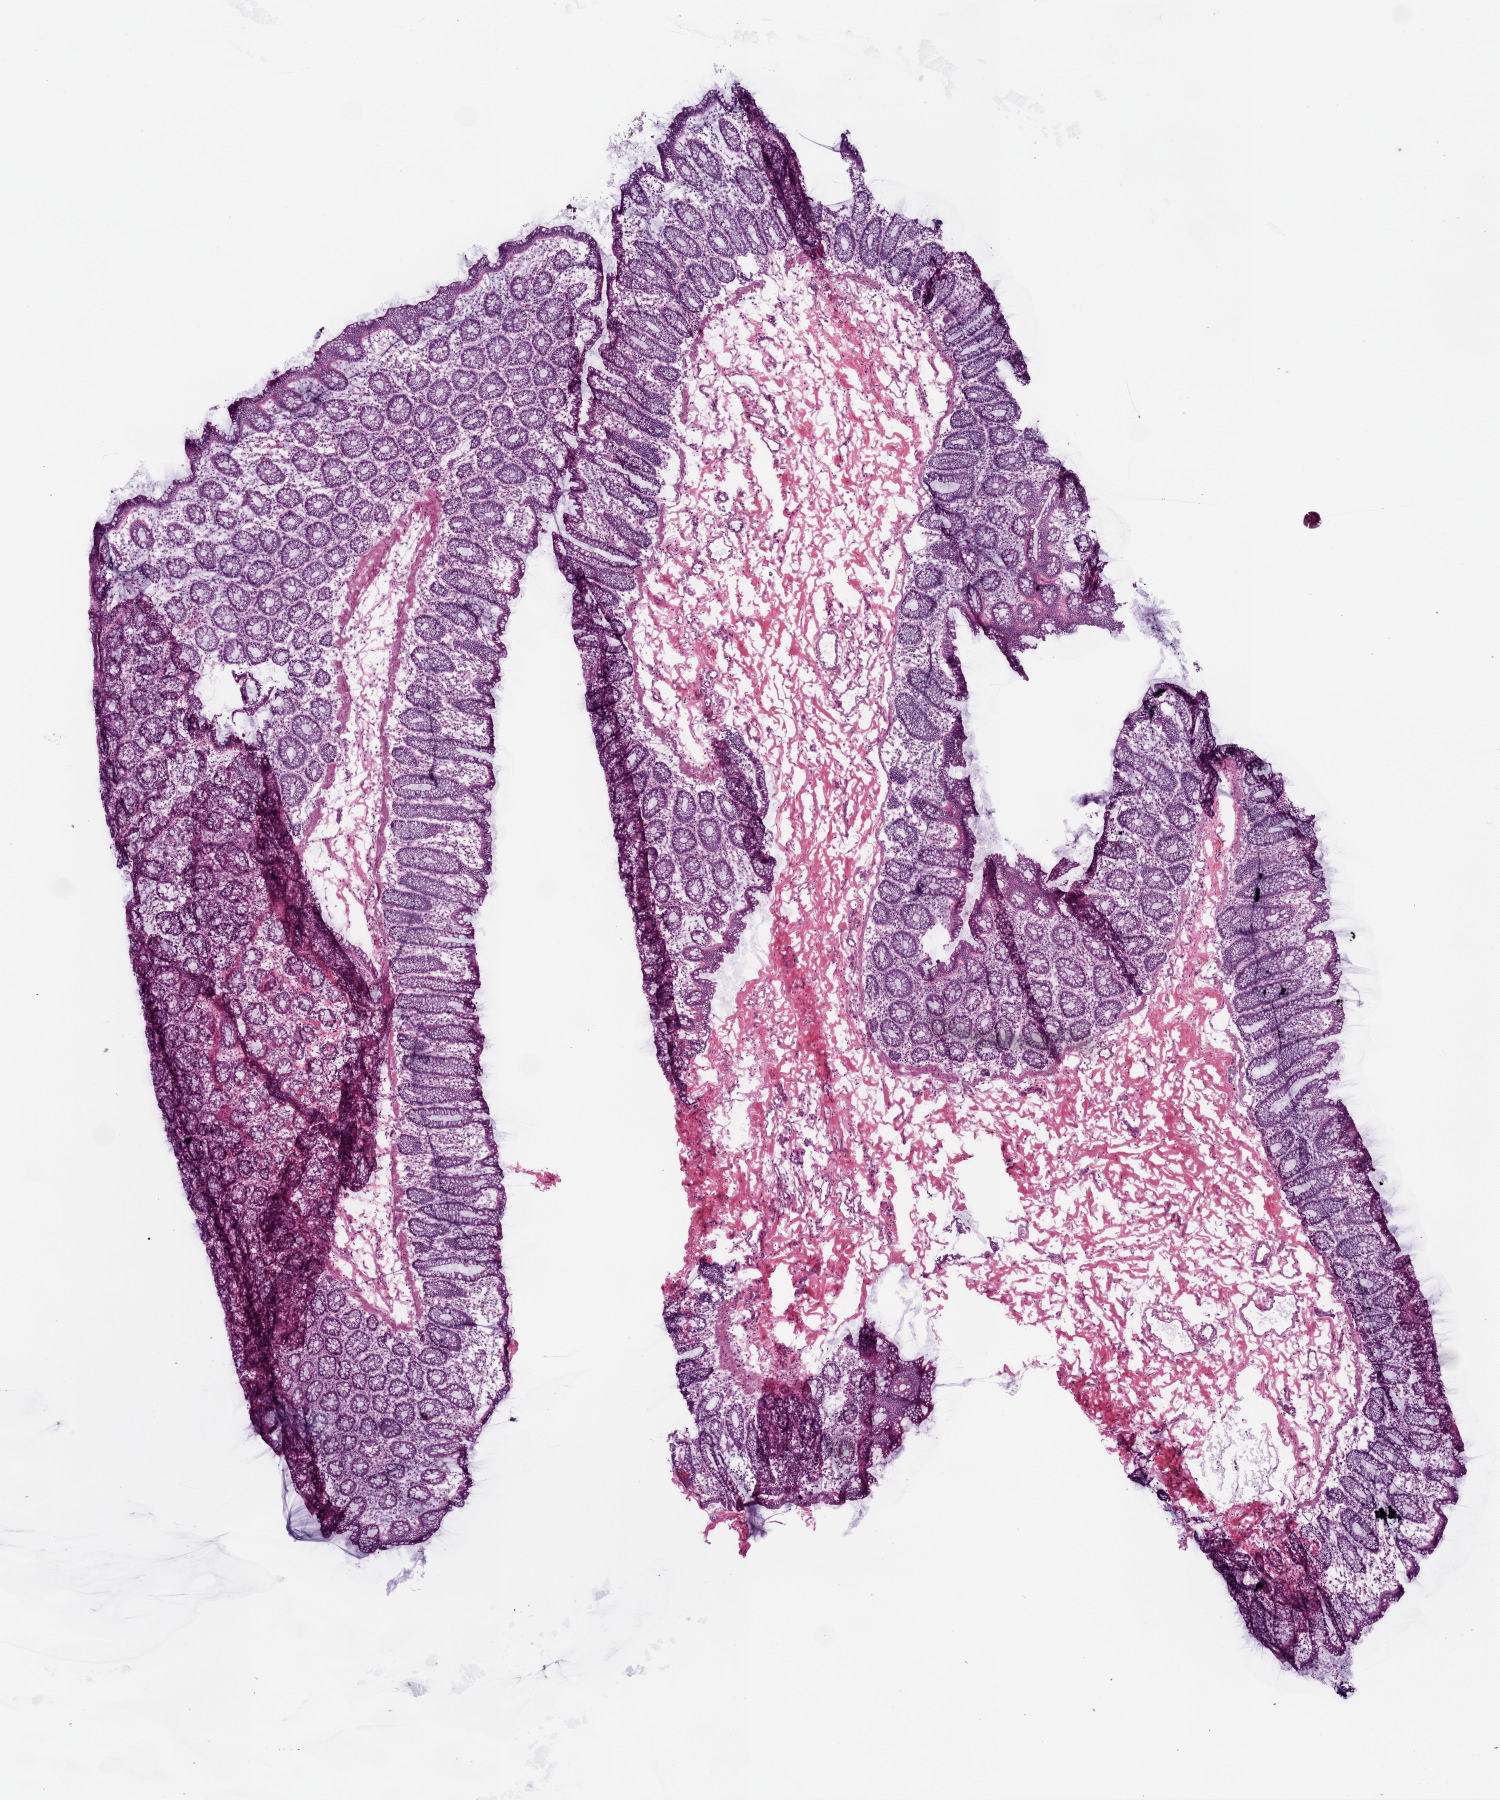
Hematoxylin and eosin (H&E) stained whole-slide image — whole scanned area (about 6.0 x 7.2 mm, slide scanned at 20x) shown as a low-resolution overview, frozen section from the top of the tissue portion, colon, solid tissue normal (non-tumour tissue) sample. Patient: male, age at initial diagnosis 87 years.
This section: solid tissue normal (non-tumour) sample from the same patient. Patient diagnosis: Adenocarcinoma, NOS (sigmoid colon).